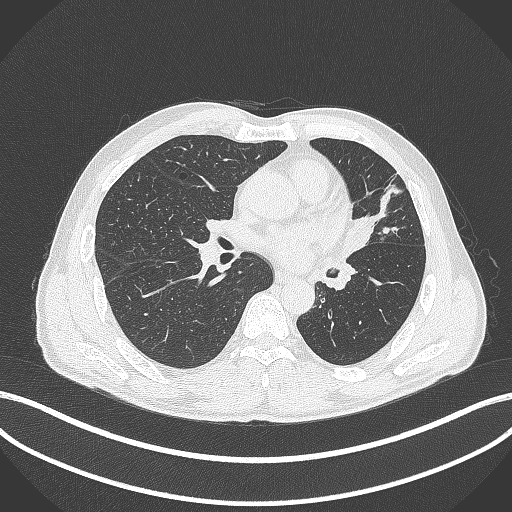
Chest CT, one axial slice. Position 218 of 429 along the scan axis. Reconstruction kernel B70f. Lung window (W 1500 / L -600 HU). 1 mm slice thickness. 512 × 512 image matrix. Male patient, age 57 years. From the clinical record (not read from this slice): clinical TNM (as recorded): T2b N0 M0.
Annotated regions visible in this slice (rectangle marked by the reading radiologist):
- lung tumour (recorded histology: squamous cell carcinoma): bounding box (x1, y1, x2, y2) in pixels: (341, 208, 374, 262)